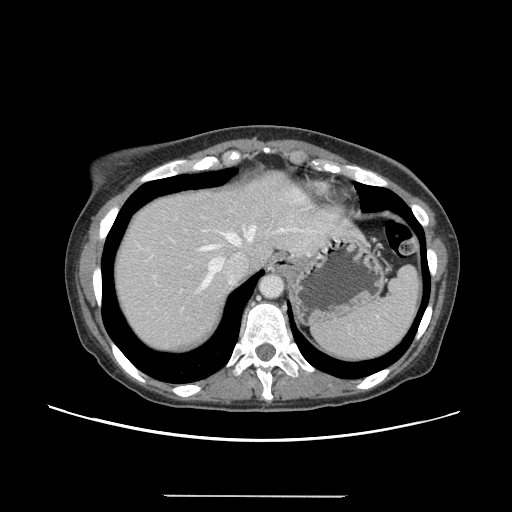
Contrast-enhanced abdominal CT, one axial slice; slice 121 of 144 in the series (ordered by position); intravenous contrast given; soft-tissue window (W 400 / L 40 HU); 2.5 mm slice thickness; 512 × 512 image matrix, field of view 380 × 380 mm. Female patient, age 53 years. Case-level facts recorded for this patient, not image findings: diagnosis: colorectal cancer liver metastases, imaged before liver resection.
Structures marked on this image (outlined manually by an expert reader):
- hepatic veins: box from (x=198, y=226) to (x=289, y=289) px
- liver: (x=114, y=173)–(x=355, y=352)
- planned liver remnant (the part of the liver to remain after resection): (x=114, y=172)–(x=283, y=297)